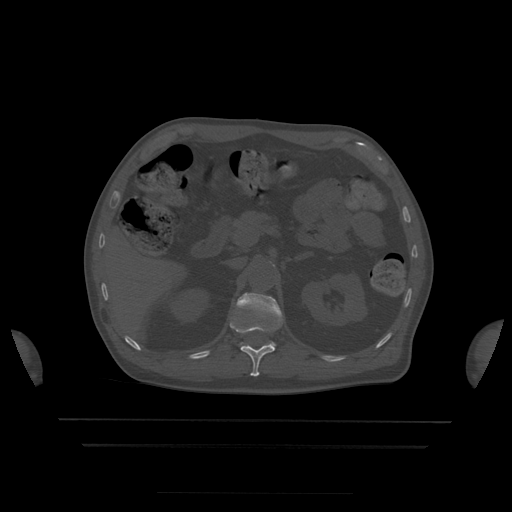
CT including the spine, one axial slice; slice 186 of 522 in the series (ordered by position); bone window (W 1800 / L 400 HU); 512 × 512 image matrix, field of view 436 × 436 mm. Patient age 68 years. Case-level facts recorded for this patient, not image findings: primary cancer: urothelial.
Annotated regions visible in this slice (semi-automatic segmentation, software-assisted and operator-edited):
- L1 vertebra: box from (x=233, y=293) to (x=282, y=347) px
- T12 vertebra: (x=230, y=322)–(x=275, y=377)